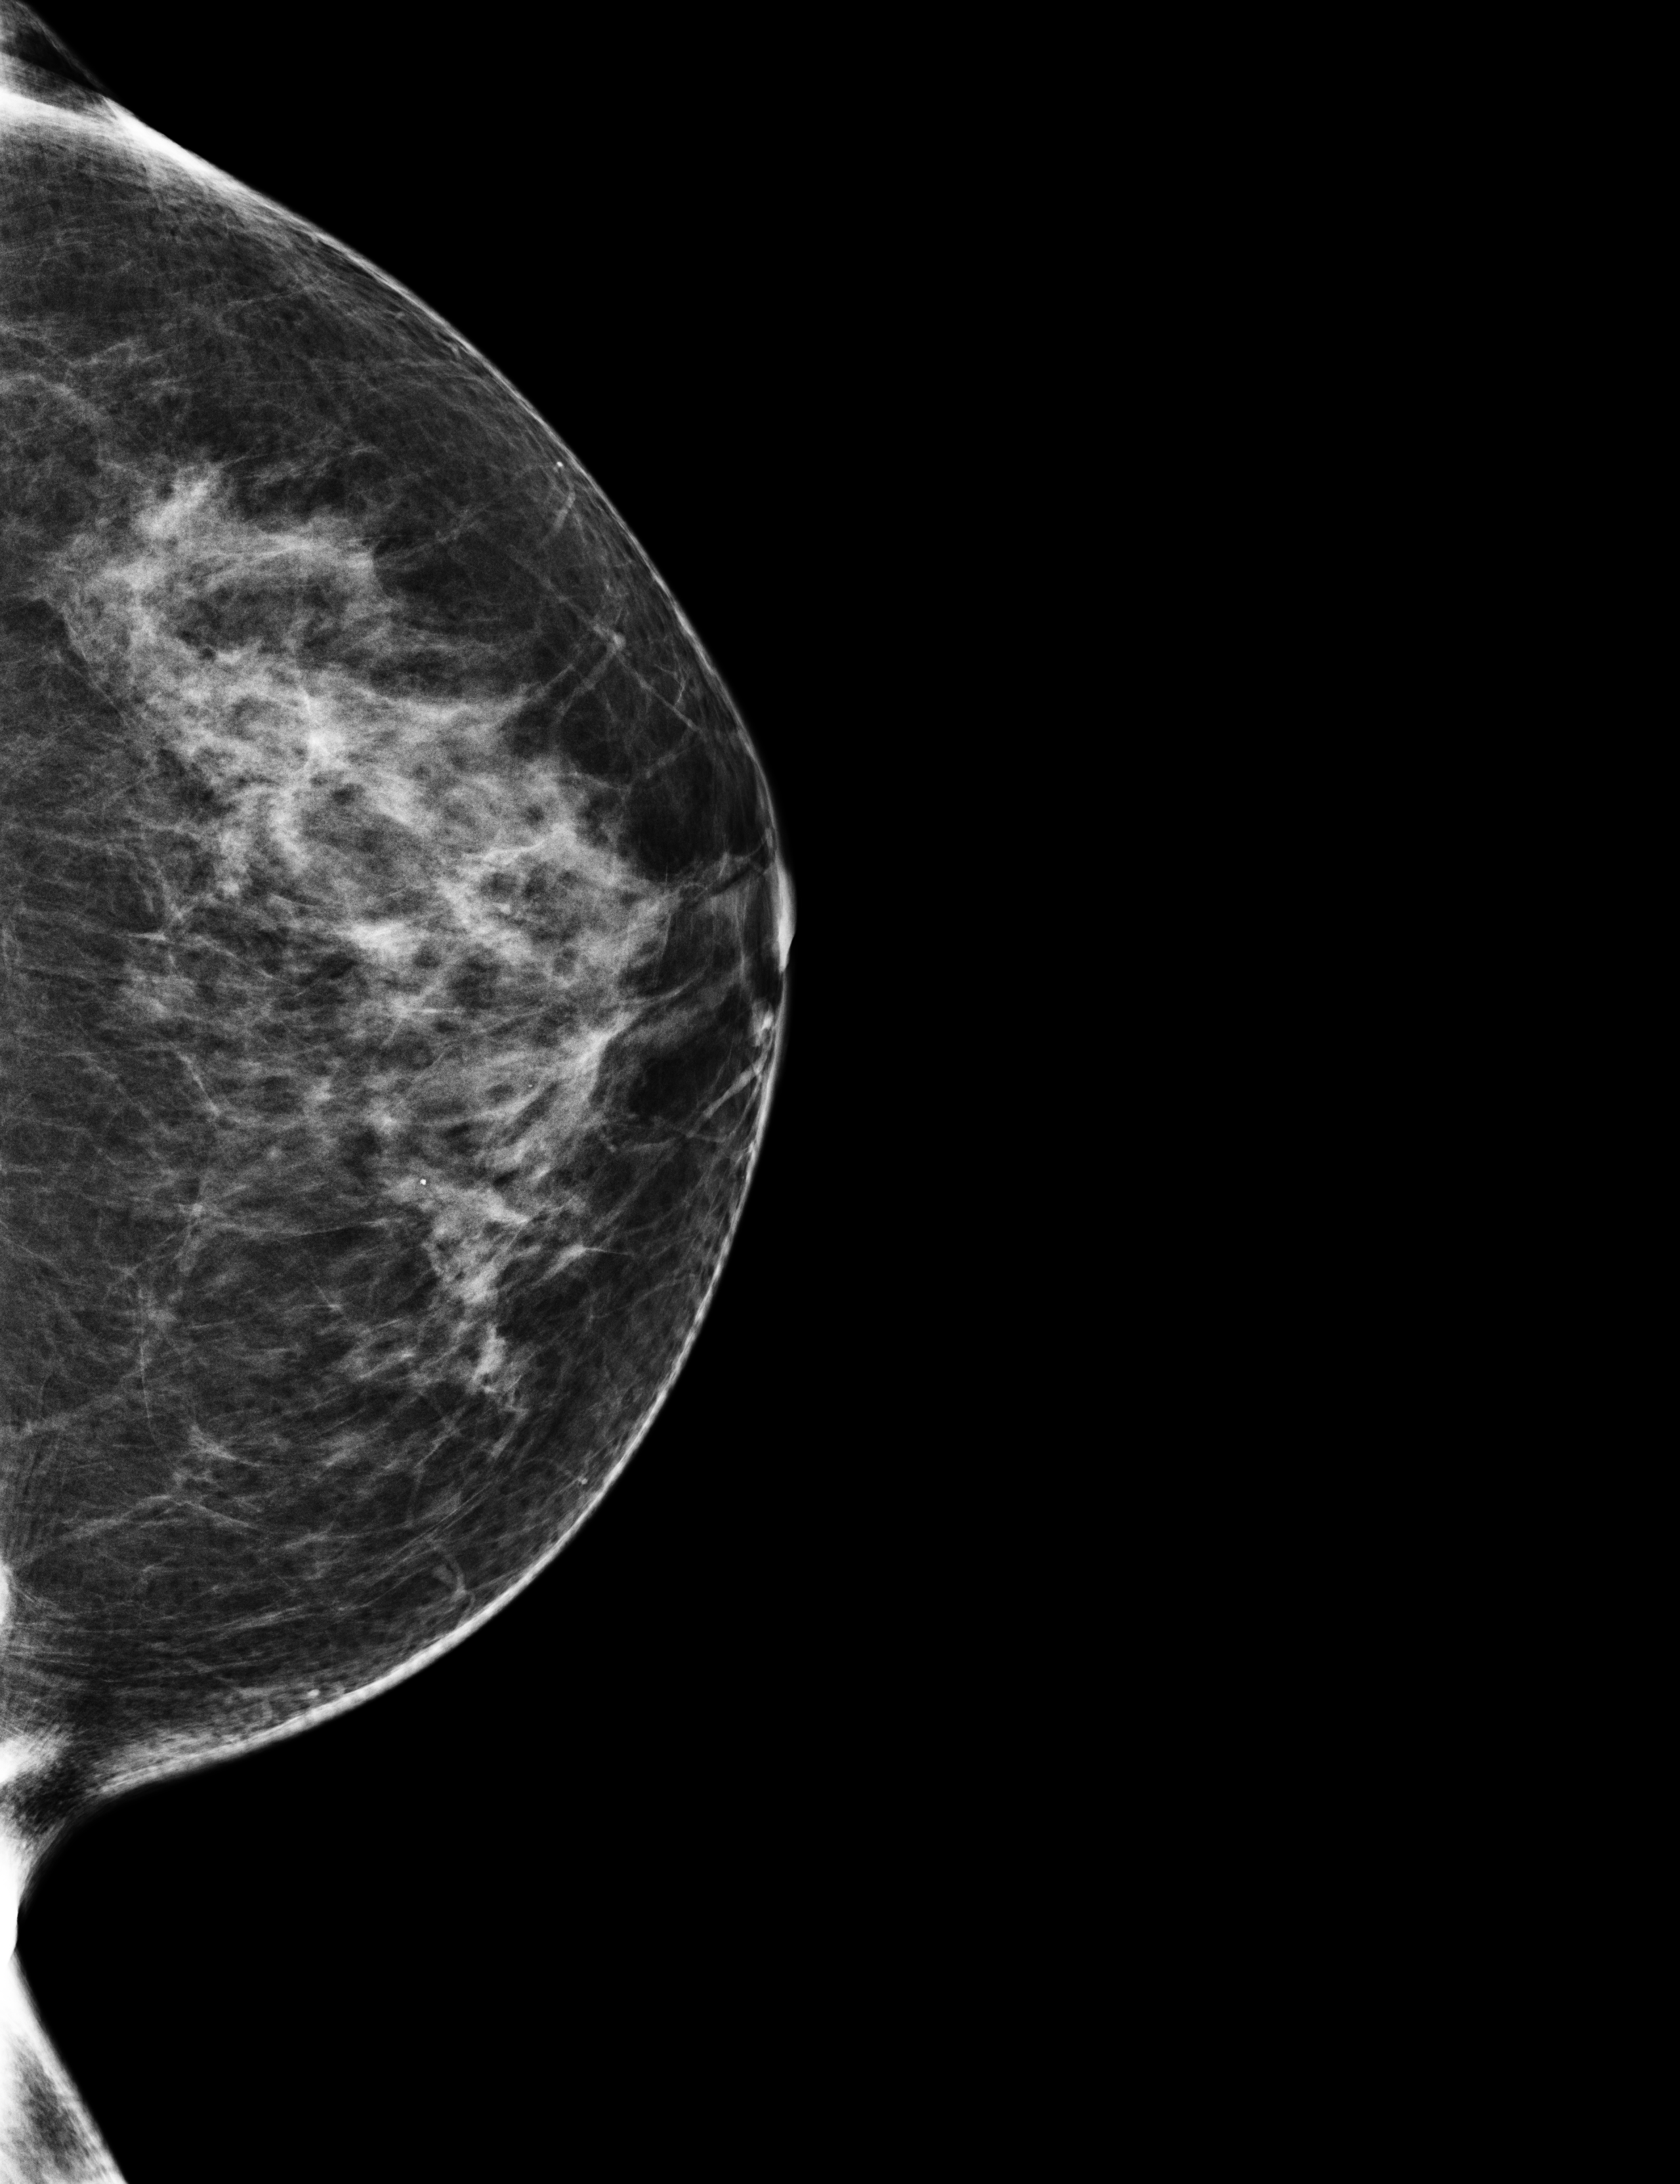
Screening examination; system: Selenia Dimensions. Female patient, age 55 years.
Image type: full-field digital mammogram. Breast: left. Projection: CC view.